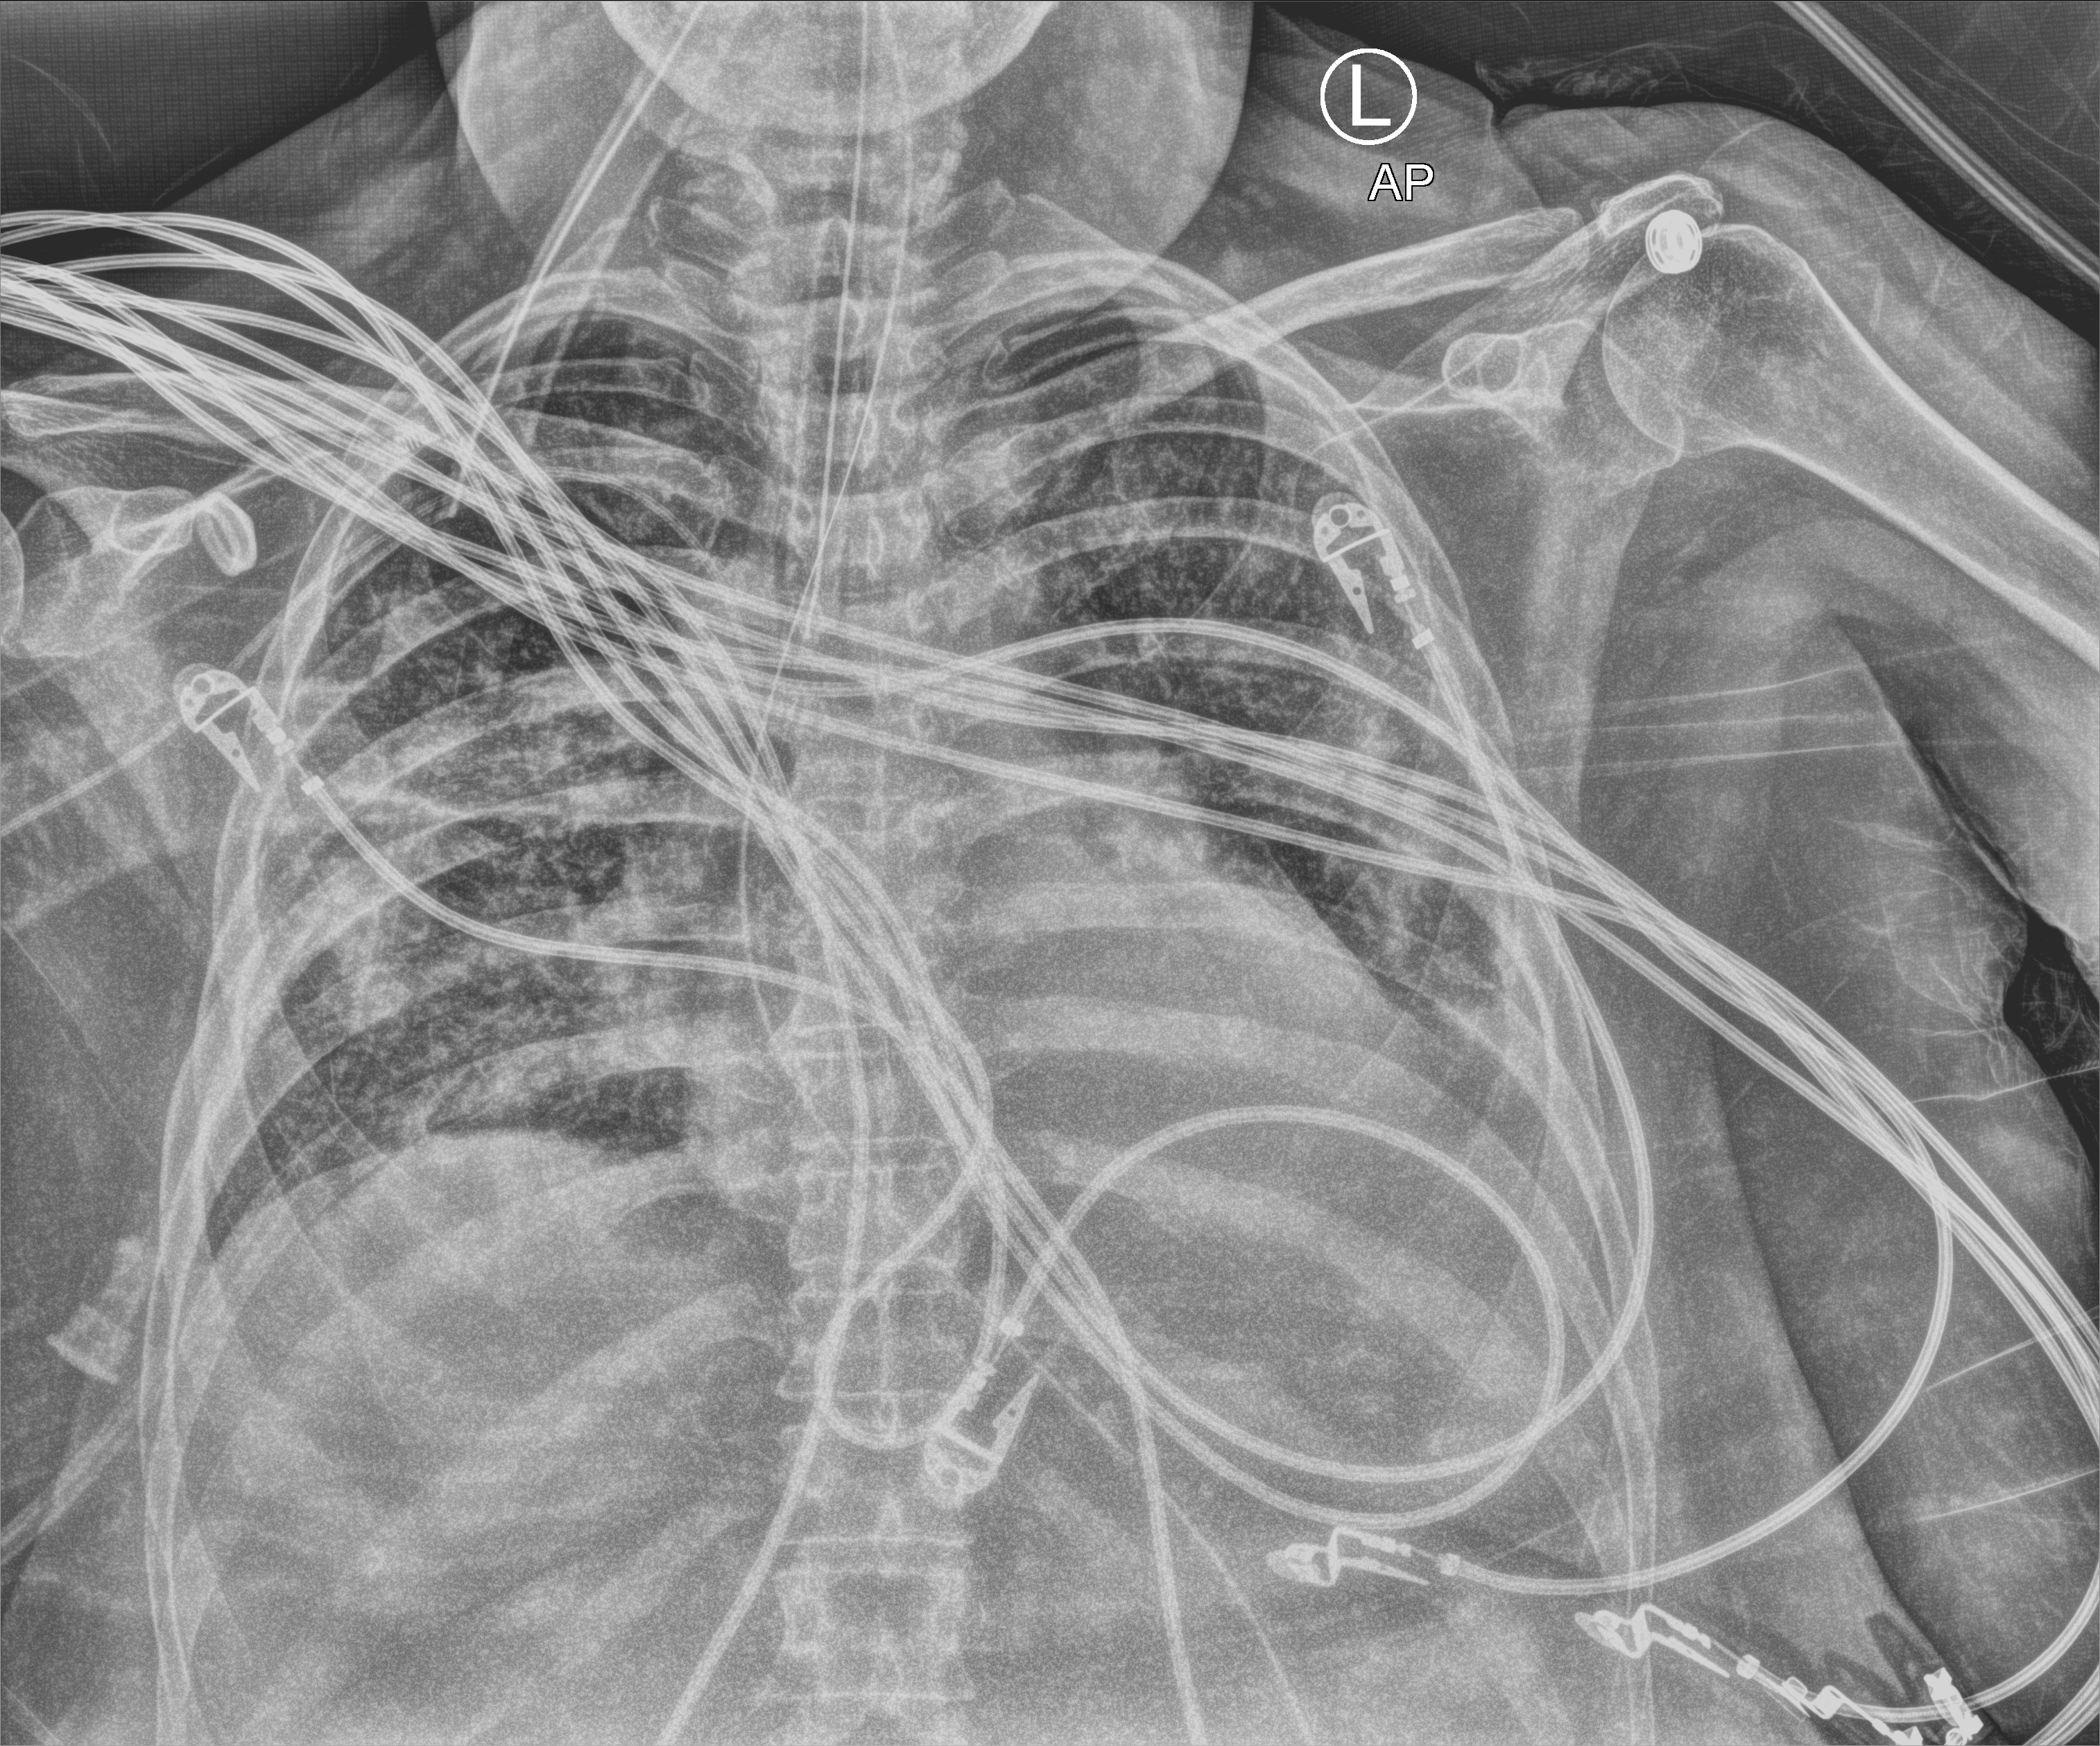
Bedside chest radiograph (computed radiography); anteroposterior (AP) projection. Female patient hospitalised with COVID-19, age 60–74 years.
From the hospital-stay record, not from the radiograph (when in the stay this image was taken is not recorded):
- admitted to intensive care during this hospital stay: yes
- length of hospital stay: 9 days
- mechanically ventilated during this hospital stay: yes